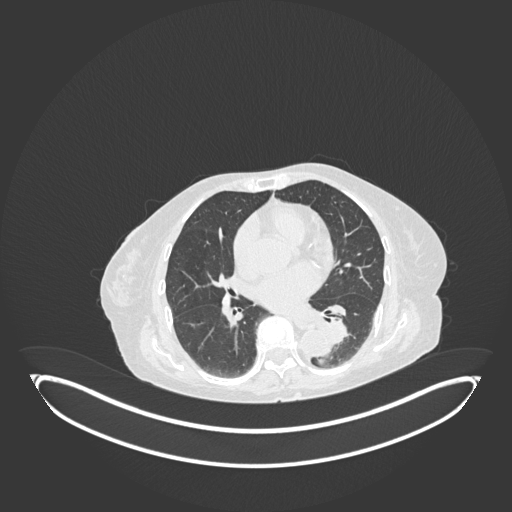
Chest CT, one axial slice. Position 55 of 189 along the scan axis. Lung window (W 1500 / L -600 HU). 512 × 512 image matrix, field of view 500 × 500 mm. Female patient, age 82 years. Case-level facts recorded for this patient, not image findings: clinical TNM (as recorded): T1b N0 M1.
Outlined on this slice (rectangle marked by the reading radiologist):
- lung tumour (recorded histology: adenocarcinoma): bounding box (x1, y1, x2, y2) in pixels: (314, 312, 353, 351)